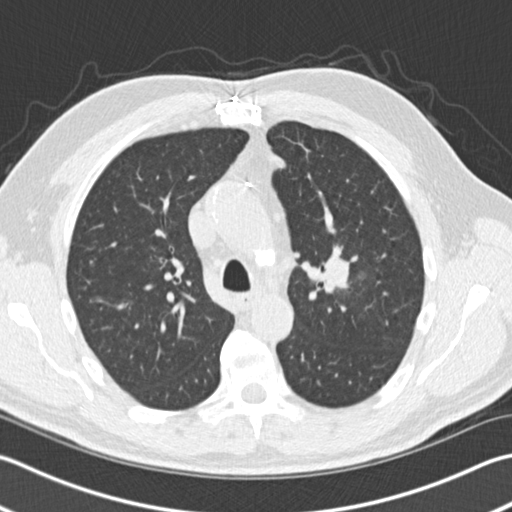
Low-dose screening chest CT, one axial slice; position 105 of 153 along the scan axis; lung window (W 1500 / L -600 HU); 2 mm slice thickness; 512 × 512 image matrix.
Annotated regions visible in this slice (manually delineated by an expert):
- lesion 1 (tumor, upper lobe of left lung): box from (x=324, y=259) to (x=347, y=289) px